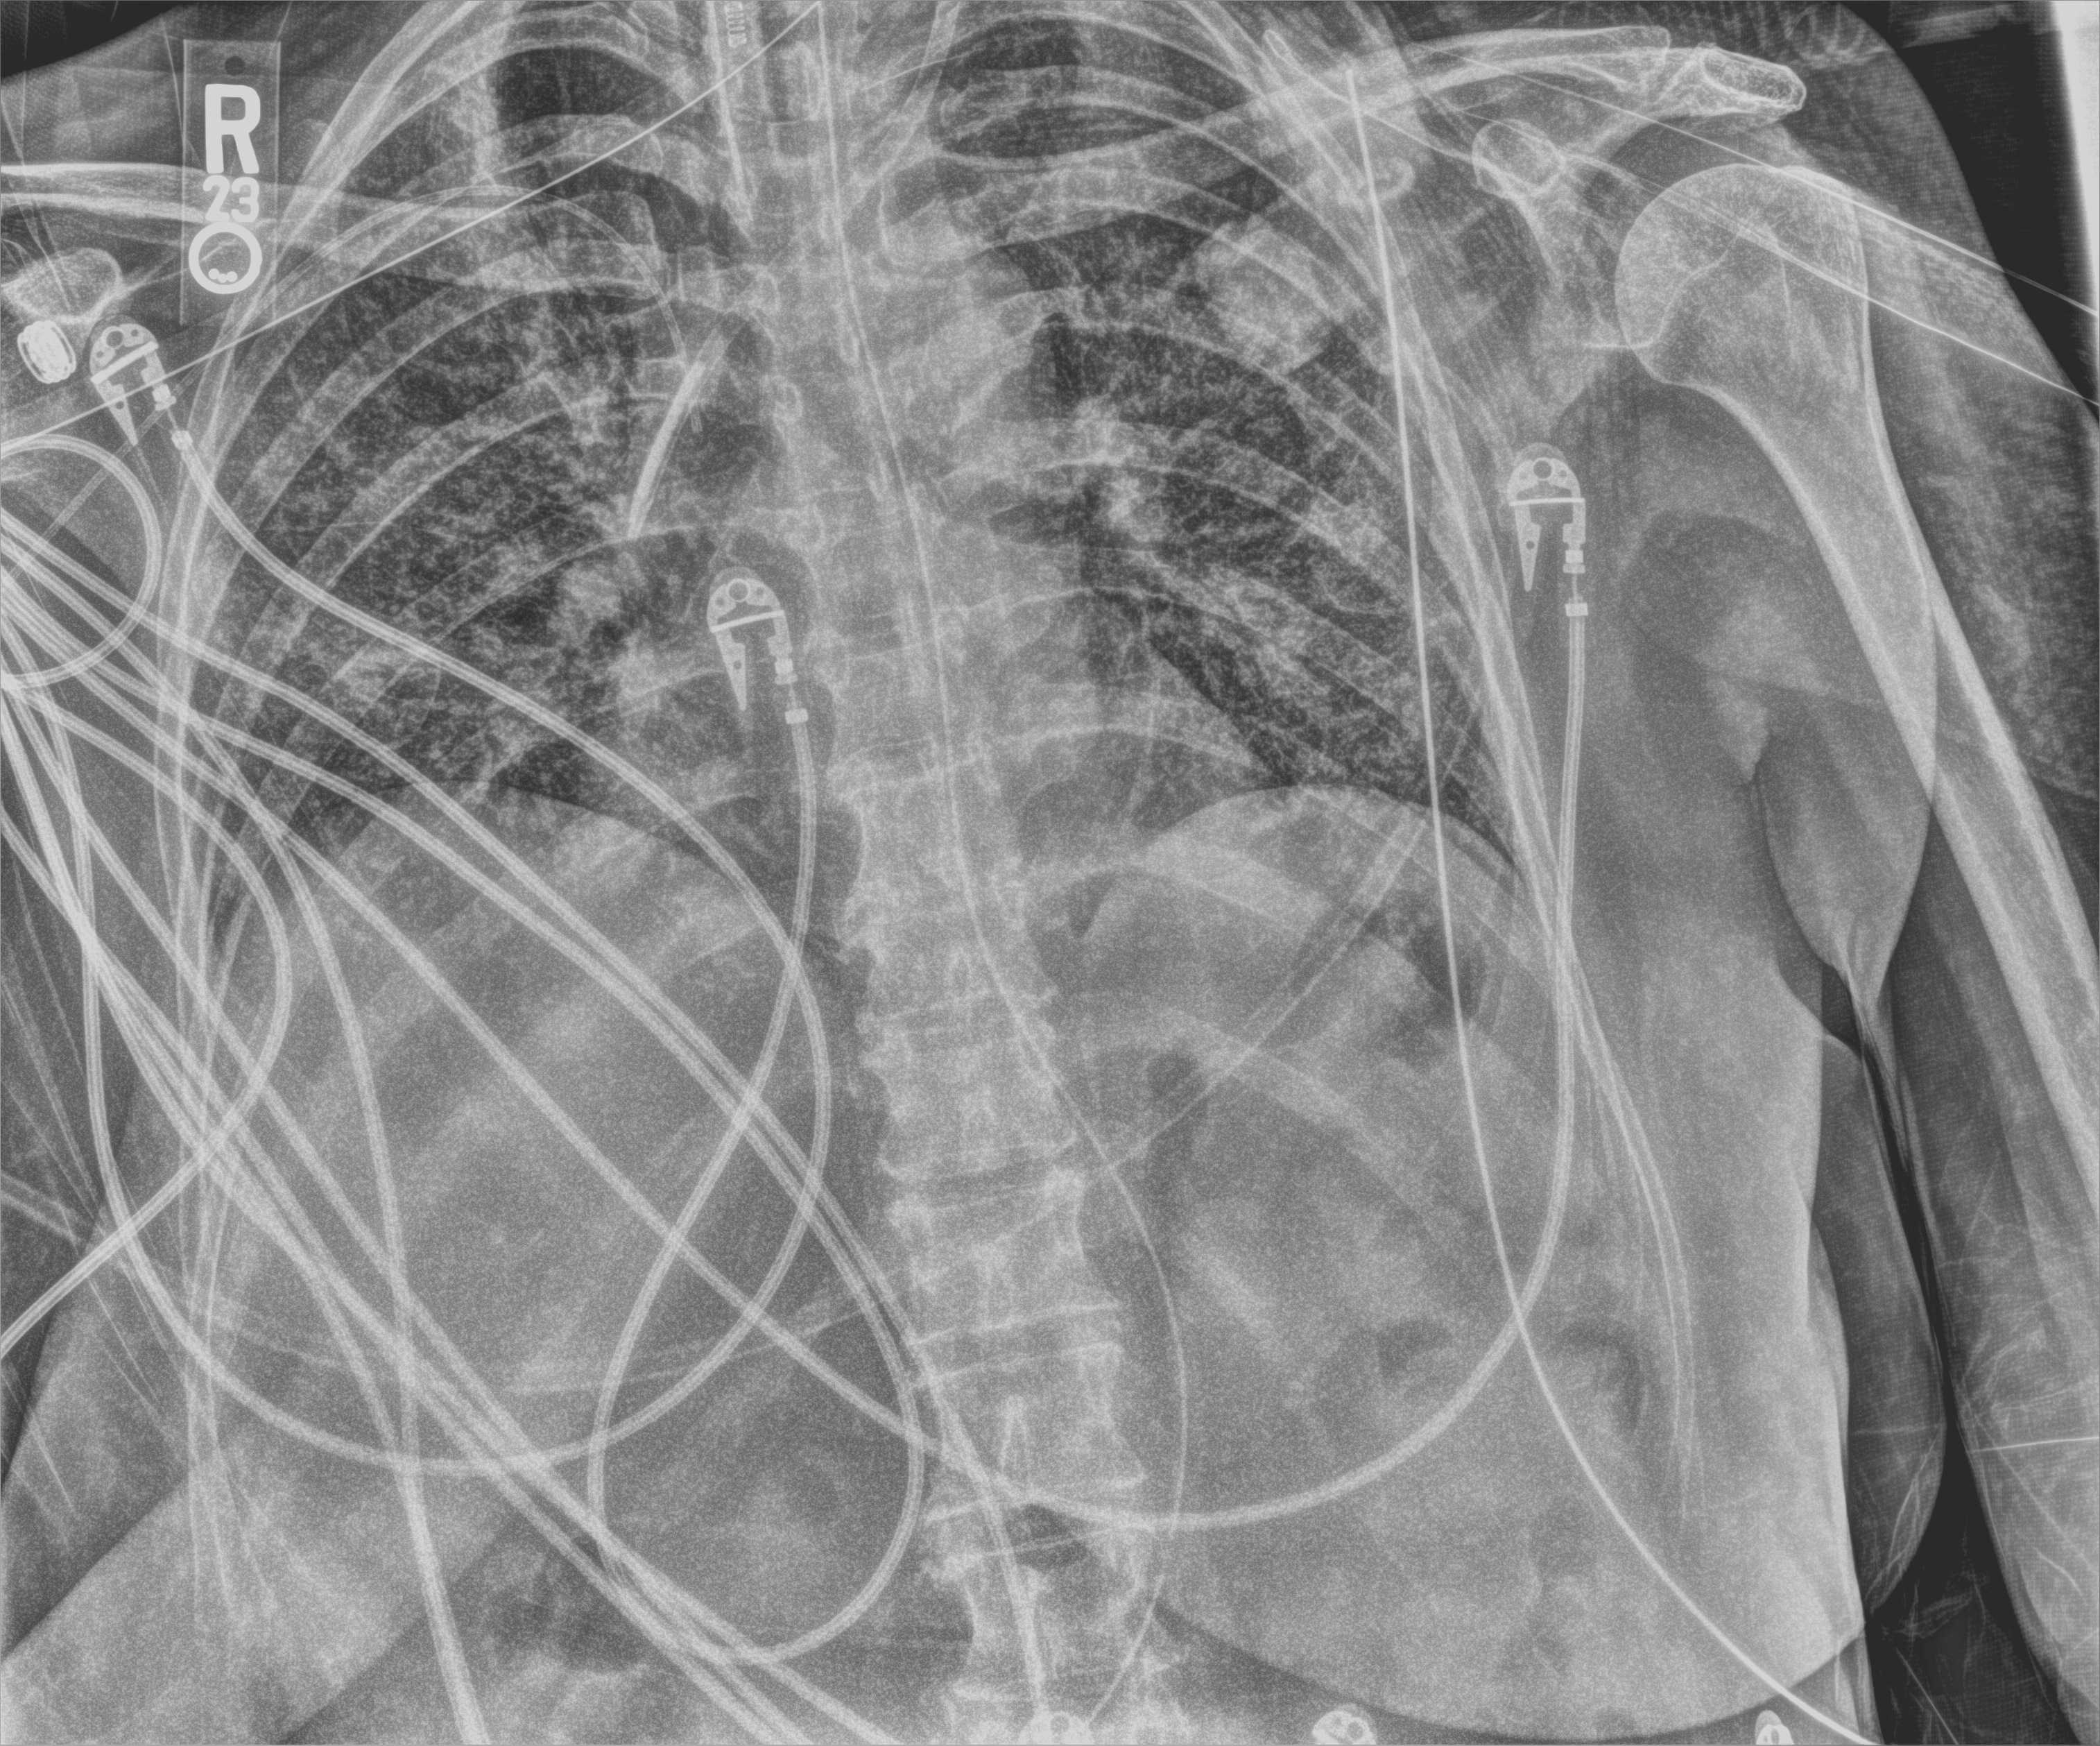
Portable chest radiograph, anteroposterior (AP) projection. Patient hospitalised with COVID-19; female, aged 60–74 years.
From the hospital-stay record, not from the radiograph (when in the stay this image was taken is not recorded):
- mechanically ventilated during this hospital stay: yes
- diabetes (admission record): no
- admitted to intensive care during this hospital stay: yes